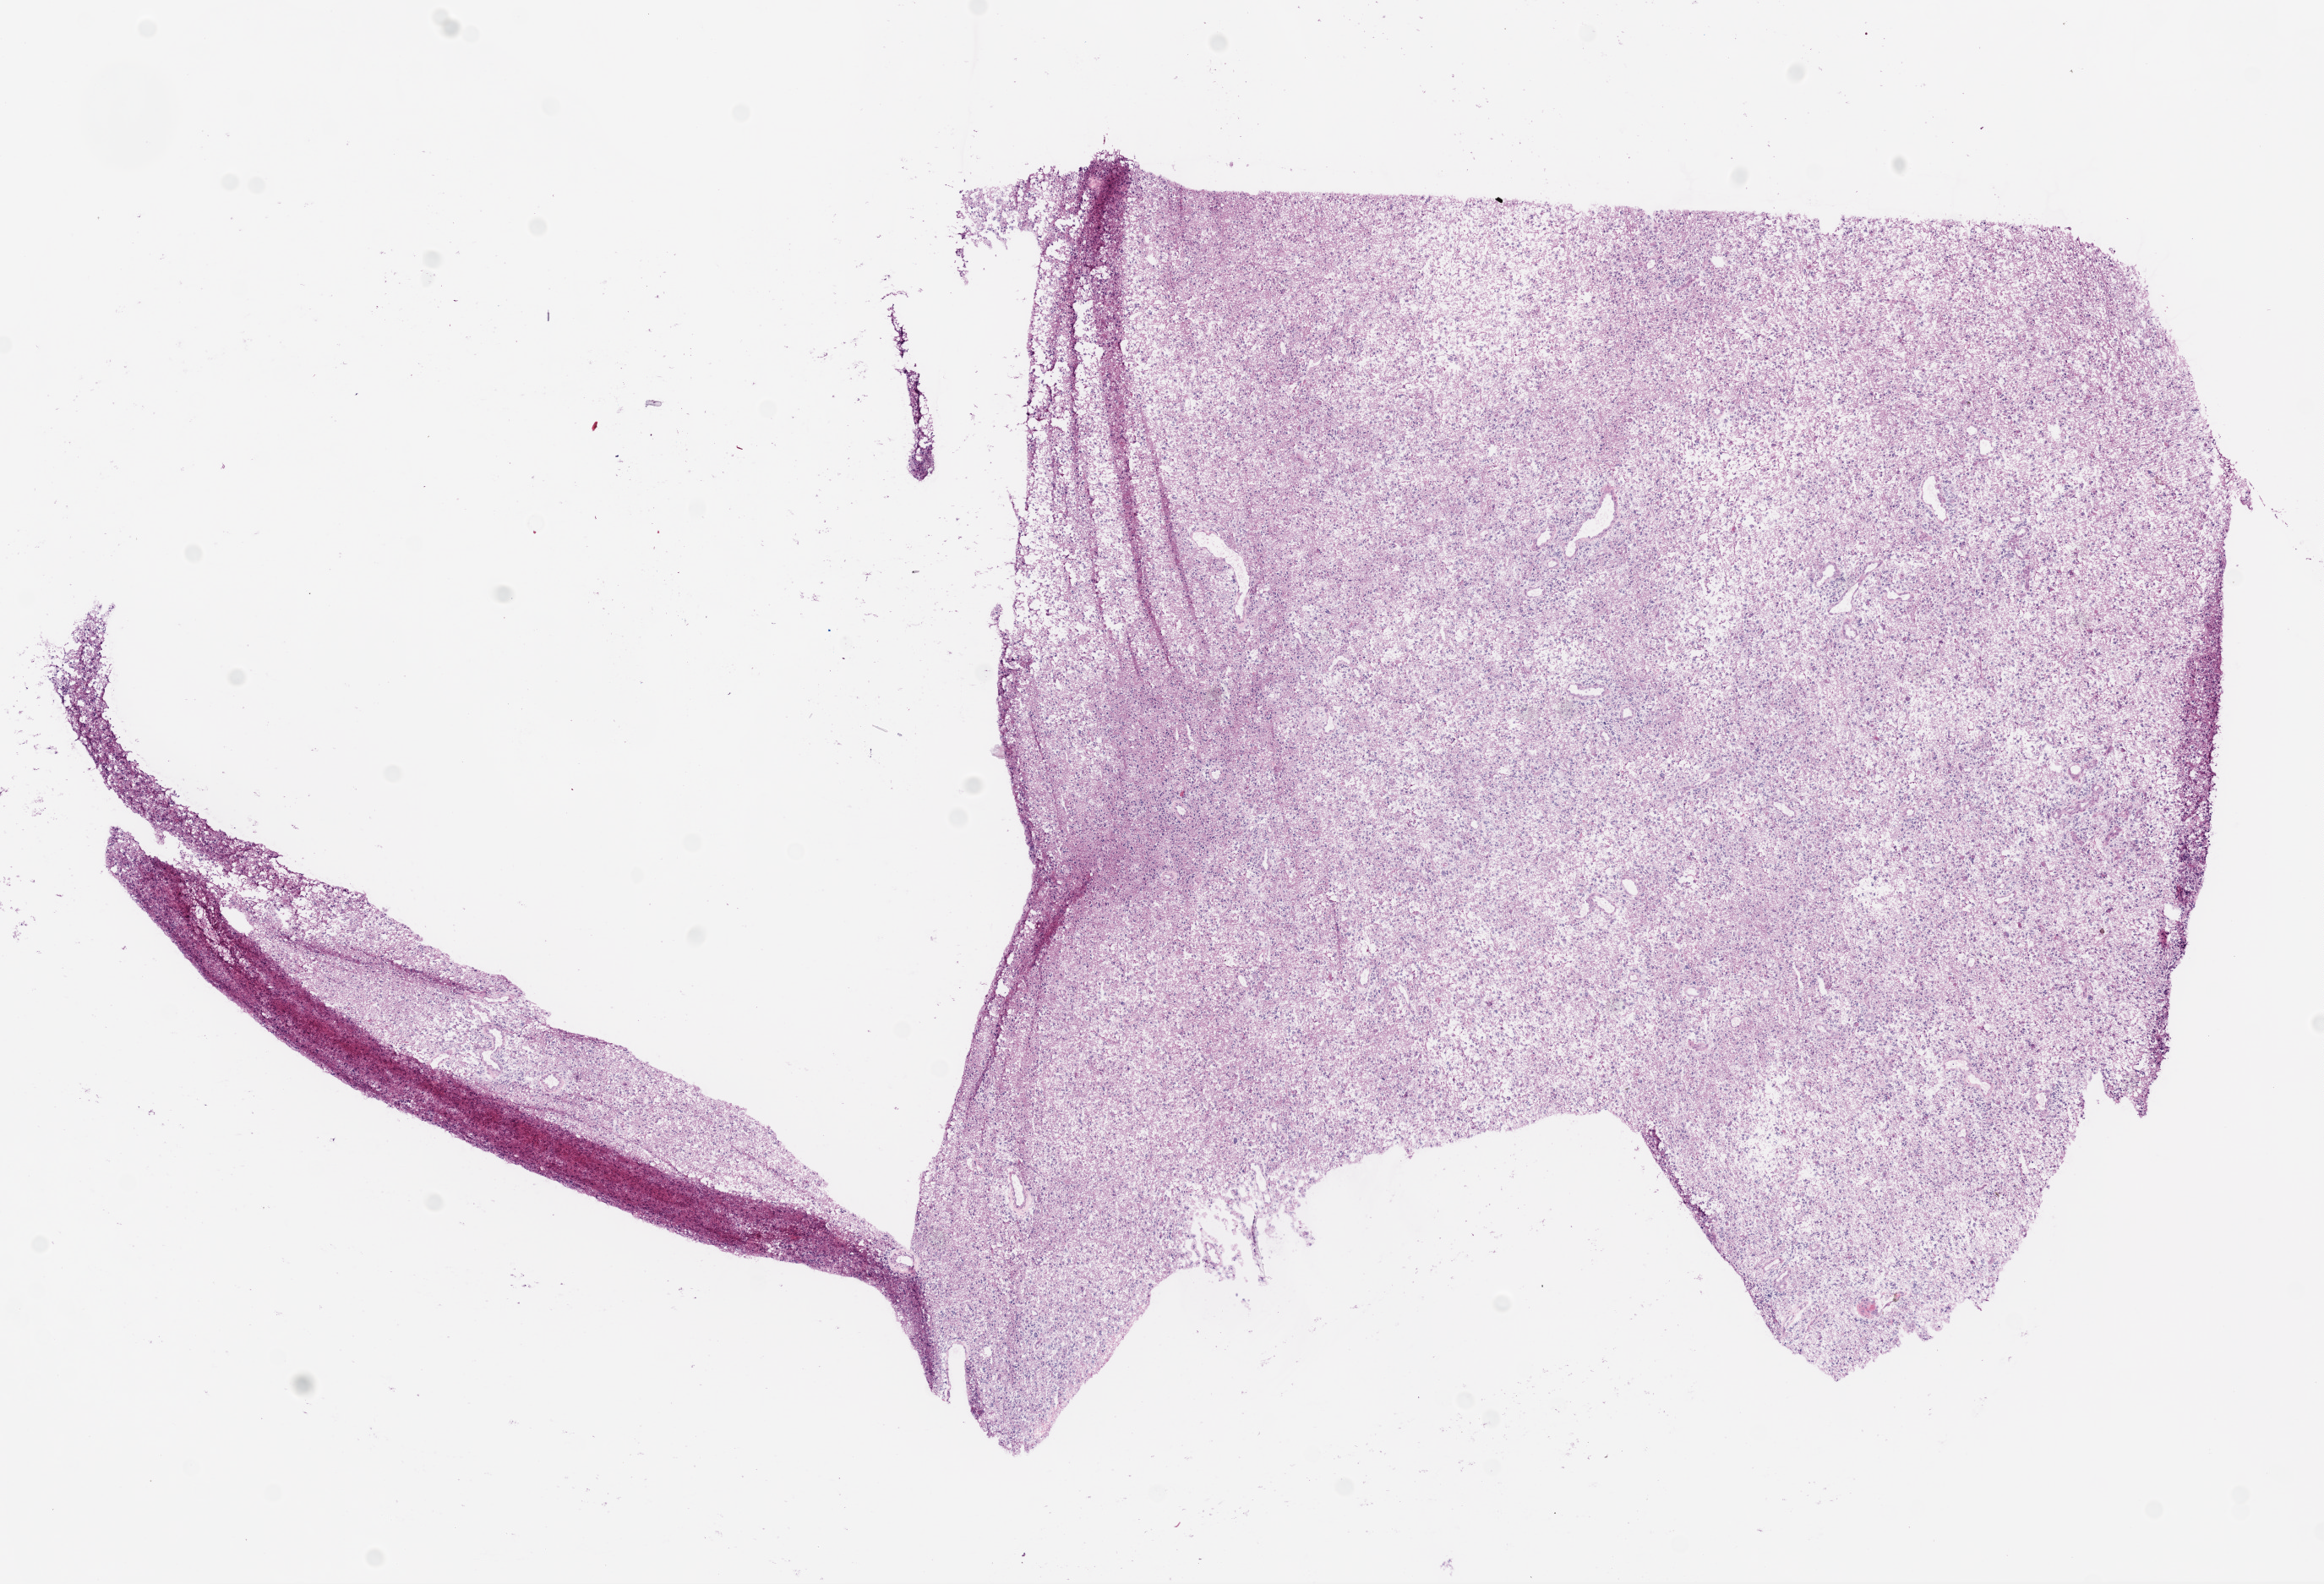
Digitized Hematoxylin and eosin (H&E) stained tissue section (whole slide) — a low-resolution overview of the entire scanned area, about 11.0 x 7.5 mm (from a 20x scan), frozen section, brain, primary tumour sample. Male patient; age at initial diagnosis 65 years.
Histologic diagnosis: Glioblastoma.